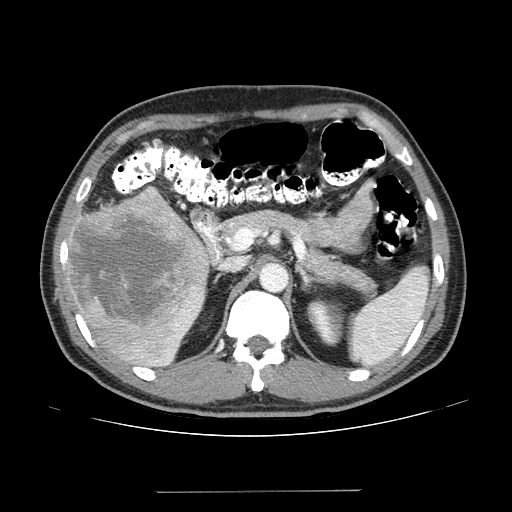
Contrast-enhanced abdominal CT (liver protocol), one axial slice. Slice 77 of 131 in the series (ordered by position). Reconstruction kernel STANDARD. 100 kVp. One of 2 acquisitions stored at this slice position. Soft-tissue window (W 400 / L 40 HU). 512 × 512 image matrix, field of view 380 × 380 mm. From the clinical record (not read from this slice): diagnosis: hepatocellular carcinoma (patient treated with transarterial chemoembolisation; whether this scan precedes or follows treatment is not stated here); TNM stage (as recorded): Stage-I; Child-Pugh class: A; tumour size: 10.3 cm.
Outlined on this slice (semi-automatically segmented with operator editing):
- liver parenchyma outside the tumour (the mass and vessels are separate outlines, so this box may not span the whole liver): bounding box [x1, y1, x2, y2] px = [64, 186, 208, 366]
- mass: [70, 188, 207, 333]
- liver vessels: [177, 310, 190, 325]